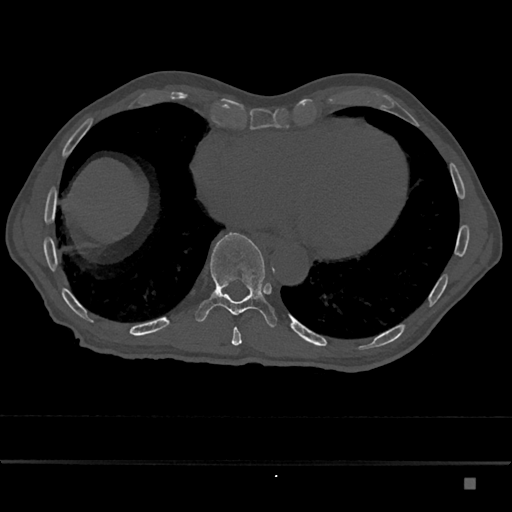
CT including the spine, one axial slice. Position 749 of 797 along the scan axis. Reconstruction kernel Br40s/3. Bone window (W 1800 / L 400 HU). 512 × 512 image matrix, field of view 390 × 390 mm. Male patient, age 72 years. Case-level facts recorded for this patient, not image findings: primary cancer: prostate.
Outlined on this slice (semi-automatic segmentation, software-assisted and operator-edited):
- T10 vertebra: box from (x=195, y=232) to (x=278, y=328) px
- T9 vertebra: (x=231, y=327)–(x=242, y=346)